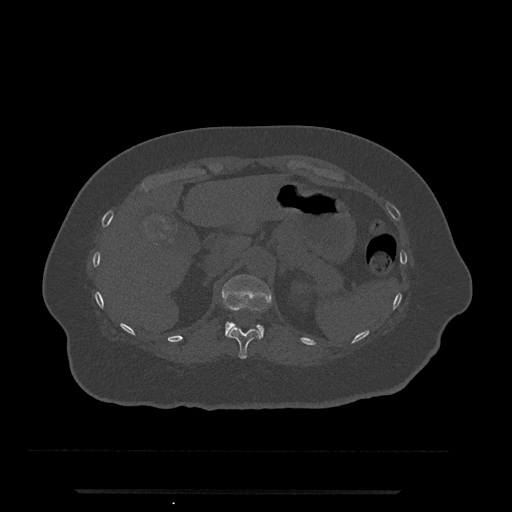
CT including the spine, one axial slice. Slice 202 of 797 in the series (ordered by position). Reconstruction kernel Br40s/3. 120 kVp. Bone window (W 1800 / L 400 HU). 0.5 mm slice thickness. 512 × 512 image matrix. Female patient, age 51 years. From the clinical record (not read from this slice): primary cancer: neuro; vertebrae with lytic lesions (as recorded): T8.
Annotated regions visible in this slice (semi-automatic segmentation, software-assisted and operator-edited):
- T11 vertebra: box from (x=226, y=327) to (x=261, y=359) px
- T12 vertebra: (x=222, y=274)–(x=272, y=338)